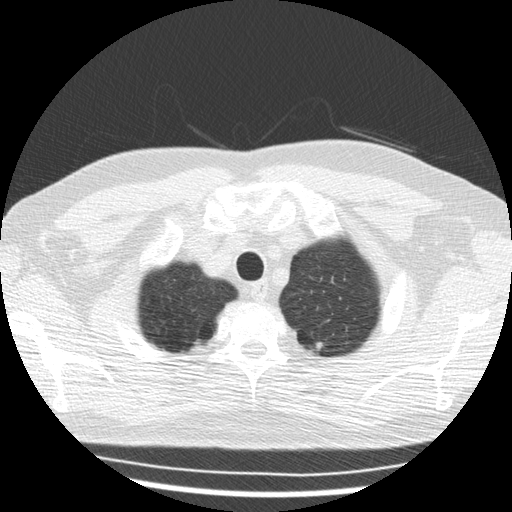
Chest CT (low-dose screening protocol), one axial image; baseline annual screen; lung window (W 1500 / L -600 HU); 2.5 mm slice thickness; standard (soft-tissue) reconstruction kernel (STANDARD); 120 kVp; slice 31 of 168 in the series. Male participant, aged 57 years at enrolment.
Expert-annotated lung lesion, bounding box (x1, y1, x2, y2) in pixels: (306, 336, 333, 359). Reader record for this screening exam (exam-level; its link to the box is not recorded): non-calcified nodule or mass ≥4 mm, right upper lobe, 7 × 6 mm, smooth margins, soft tissue attenuation. Note: the box lies in the patient's left hemithorax on this image, whereas the reader's record names the right lung; they may be different findings. Official screen result: positive, change unspecified: nodule(s) >= 4 mm or enlarging nodule(s), mass(es), or other non-specific abnormalities suspicious for lung cancer. Lung cancer was diagnosed 674 days after this screen: adenocarcinoma, NOS, left upper lobe, stage IV (AJCC 6th edition), 50 mm at pathology.